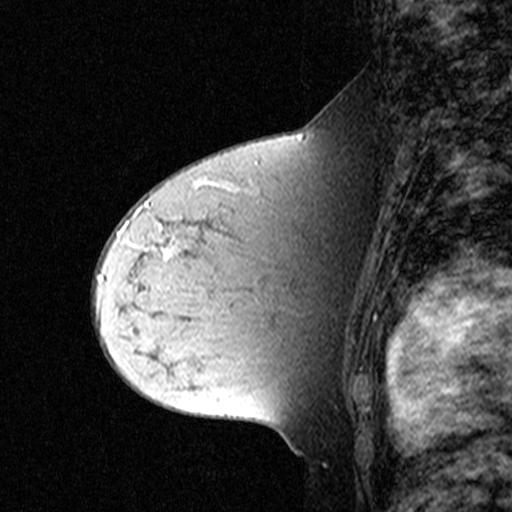
Breast MRI (dynamic contrast-enhanced), one sagittal slice; position 27 of 44 along the scan axis; dynamic contrast-enhanced study with each time point stored as its own series, time point 2 of 3 at this slice position (early post-contrast, ordered by acquisition time); 1.5 T; TE 4.5 ms, TR 11 ms; 3 mm slice thickness; 512 × 512 image matrix, field of view 200 × 200 mm. Patient: female, 44 years. Case-level facts recorded for this patient, not image findings: setting: breast cancer imaged before/during neoadjuvant chemotherapy; receptor status: triple-negative.
Structures marked on this image (semi-automatically segmented with operator editing):
- analysis volume of interest (the breast-tissue region the enhancement analysis was run in; not a lesion): bounding box [x1, y1, x2, y2] px = [132, 212, 309, 331]
- tumour enhancement mask (voxels above the 90 % enhancement threshold inside the analysis volume of interest): [164, 244, 182, 257]